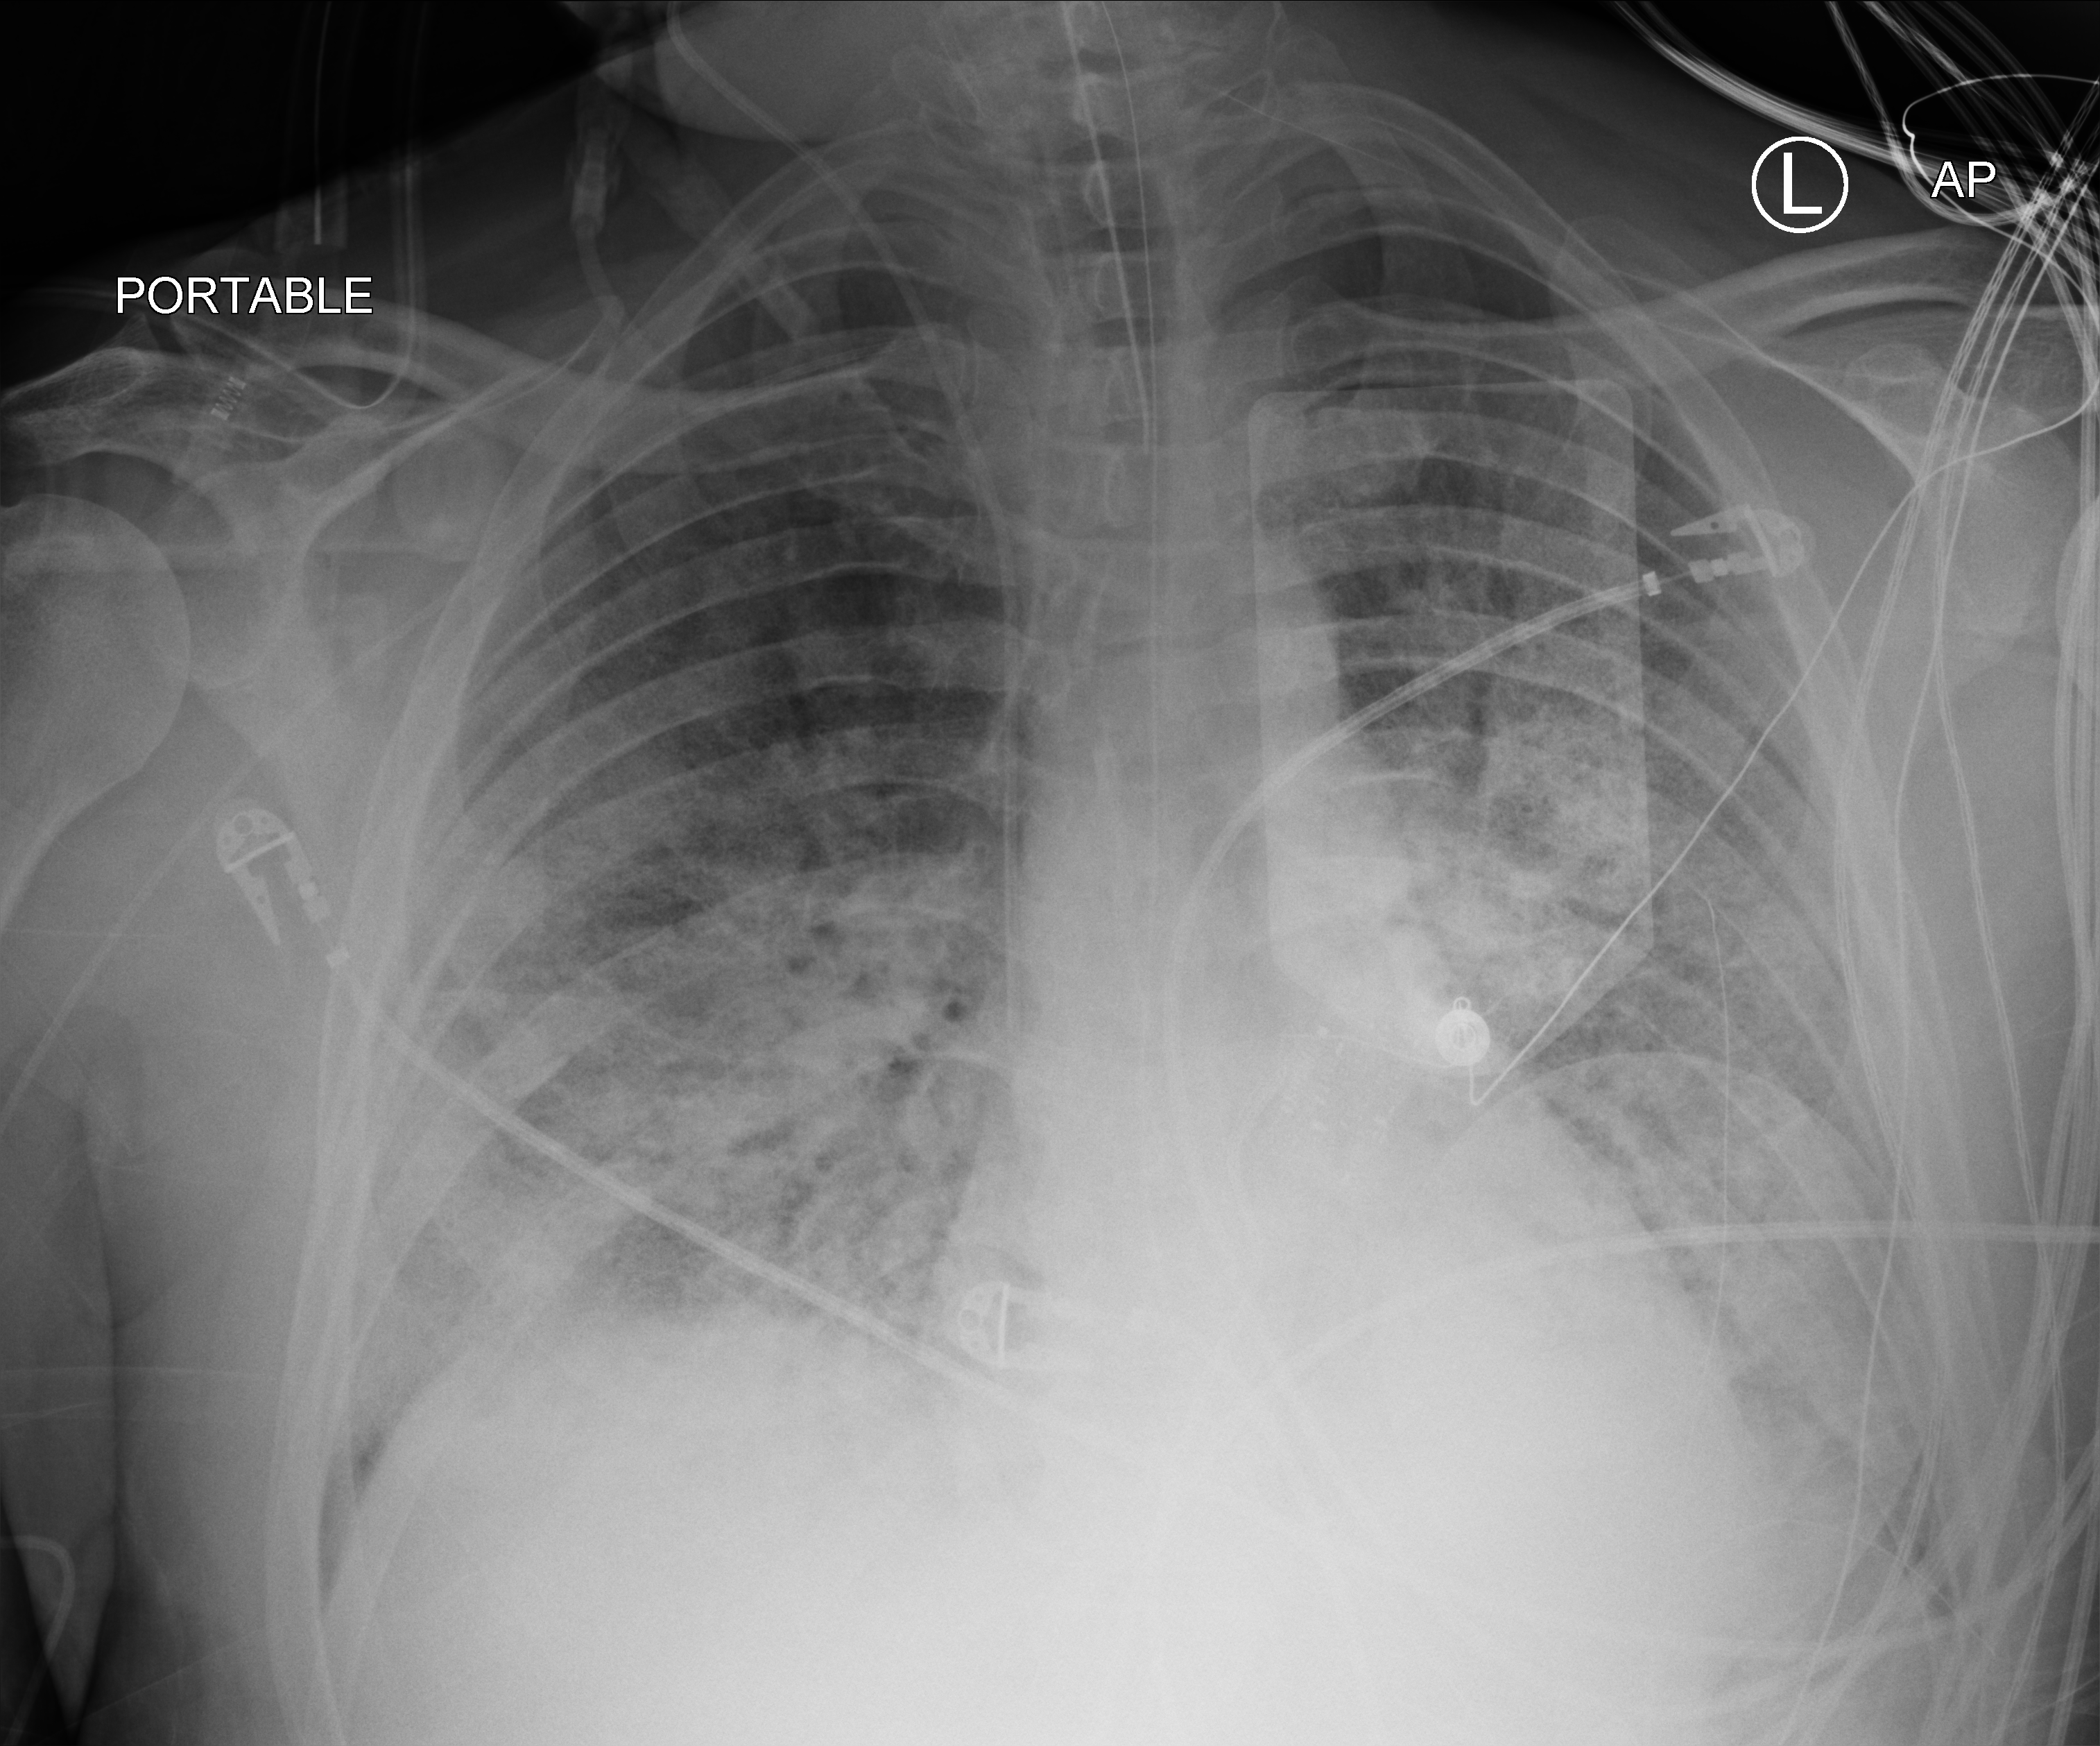
Bedside chest radiograph (computed radiography), anteroposterior (AP) projection. Male patient hospitalised with COVID-19, age 18–59 years.
Hospital-stay facts (about this admission, not read from this image; timing relative to this image not recorded):
- admitted to intensive care during this hospital stay: yes